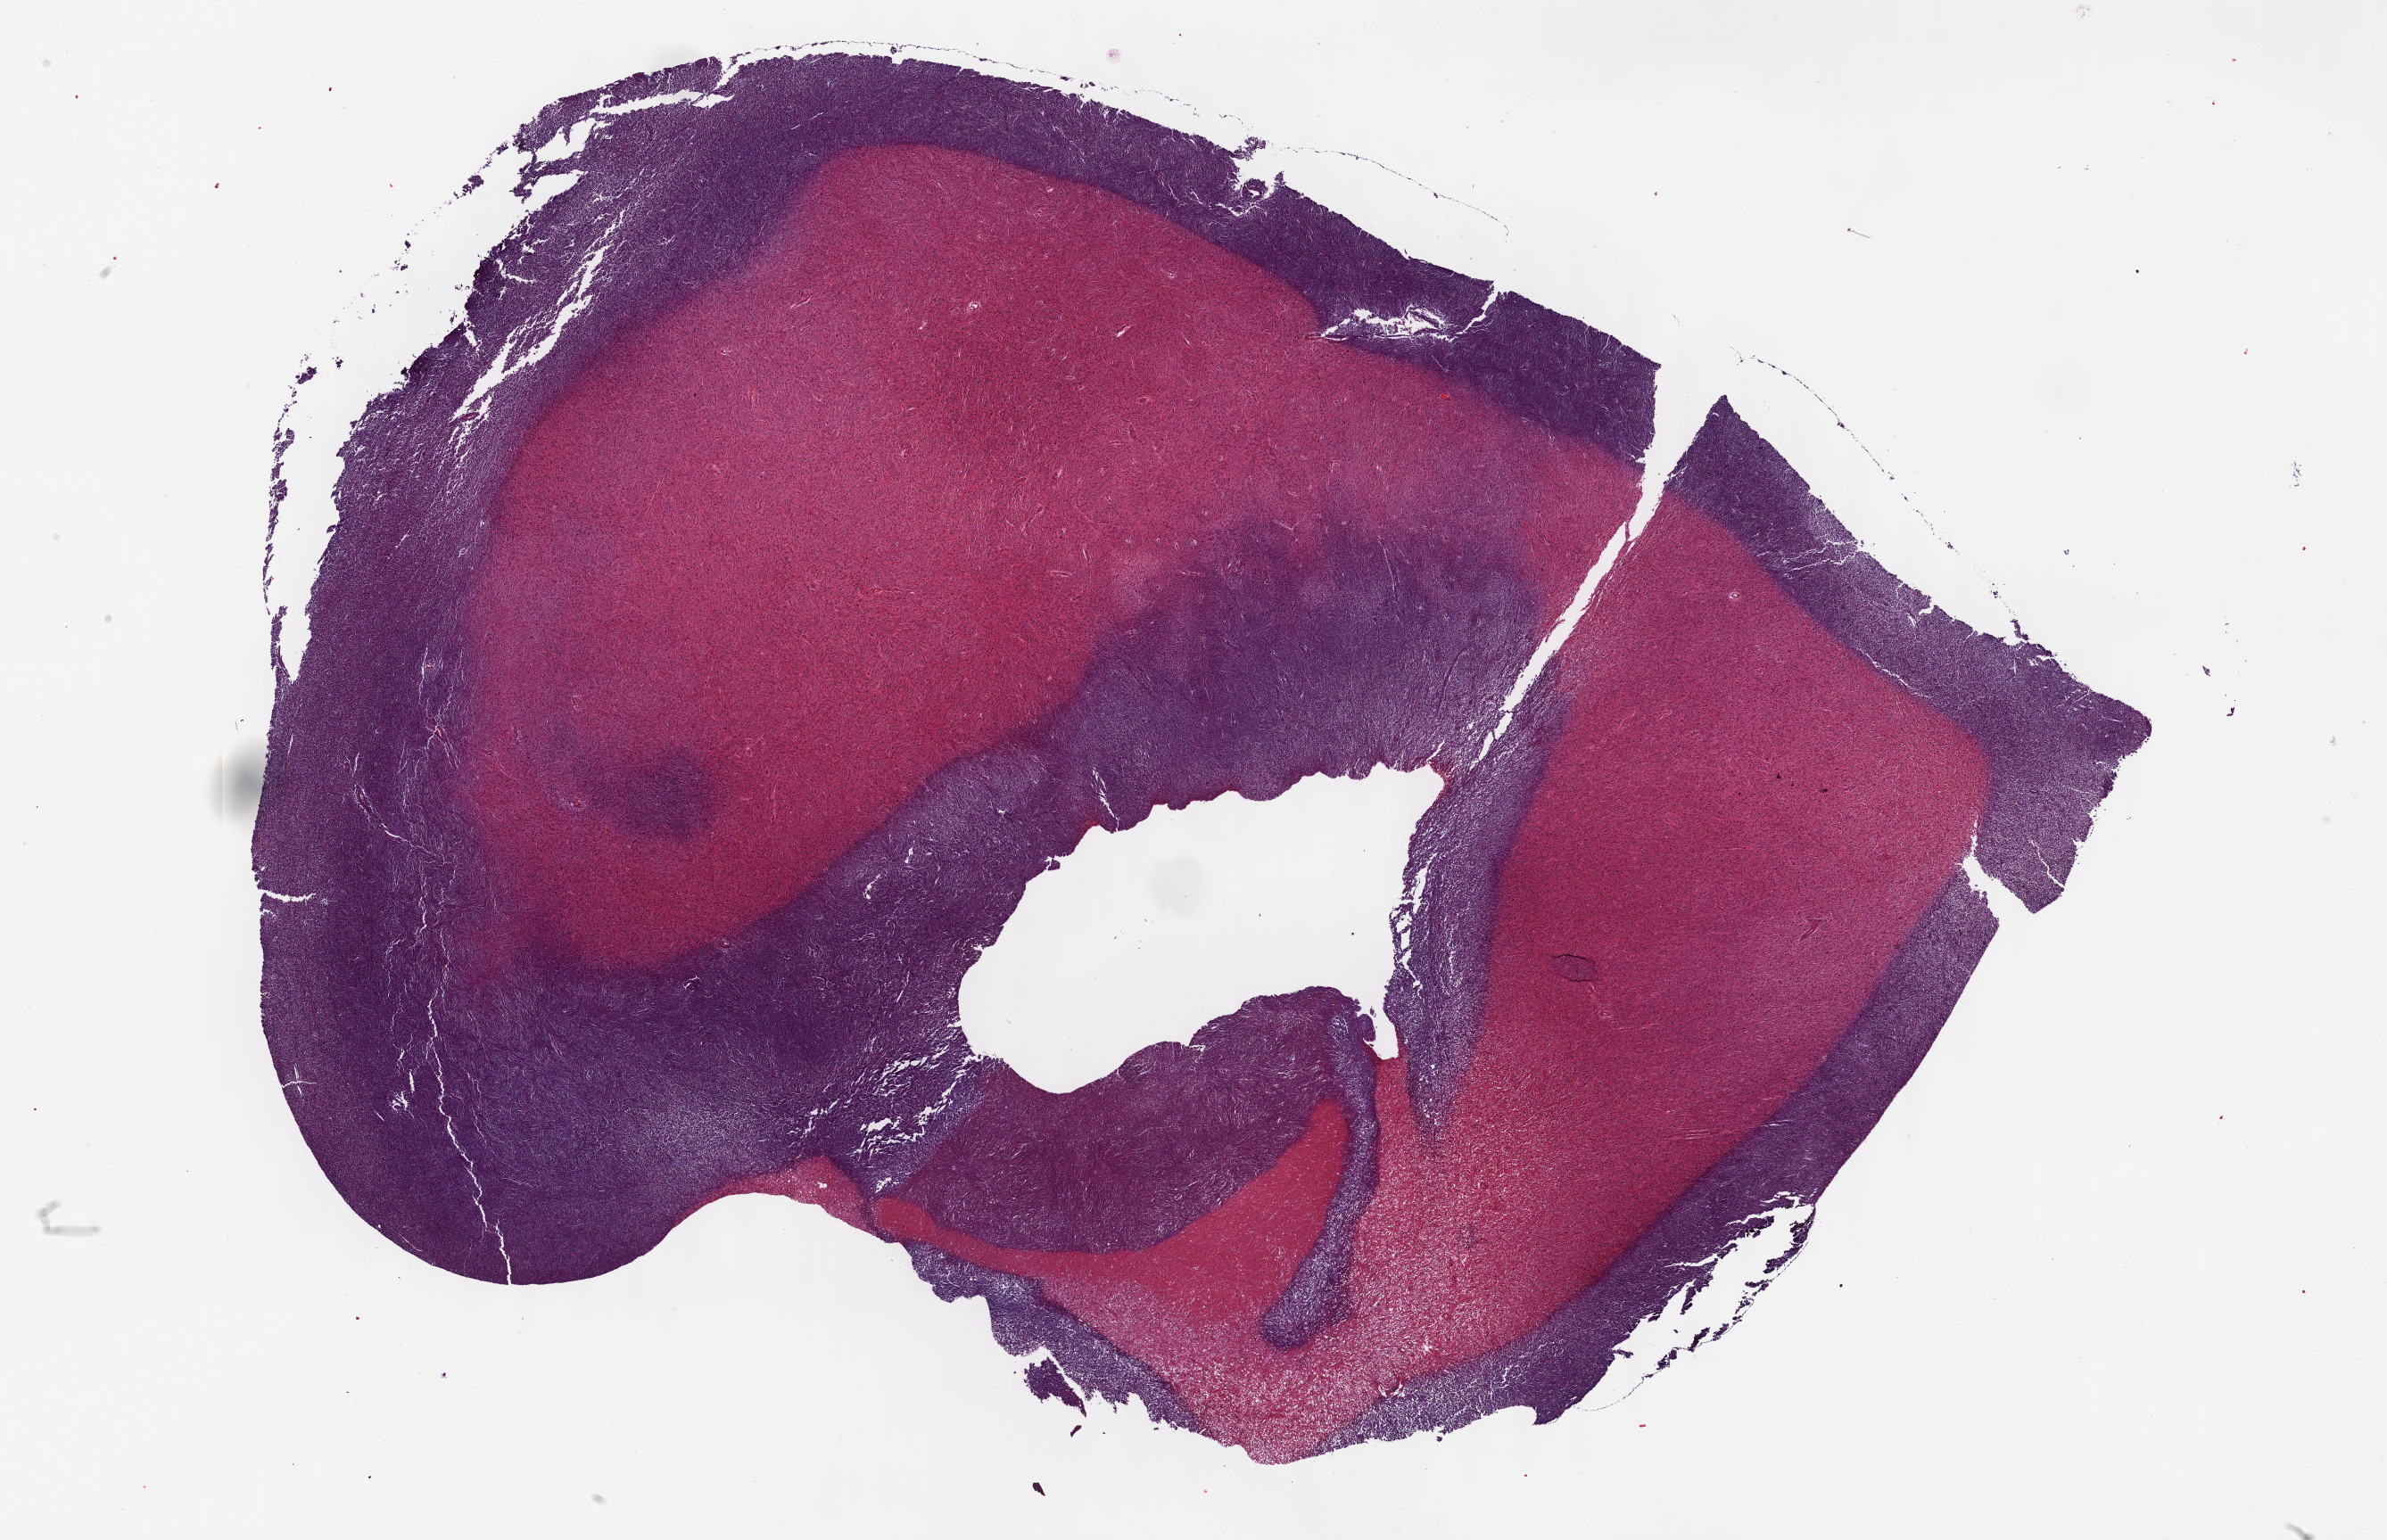
H&E-stained whole-slide image, a low-resolution overview of the entire scanned area, about 21.6 x 14.0 mm (from a 40x scan), formalin-fixed paraffin-embedded (FFPE) diagnostic section, retroperitoneum and peritoneum, primary tumour sample. Female patient; age at initial diagnosis 70 years.
- diagnosis: Dedifferentiated liposarcoma (retroperitoneum)